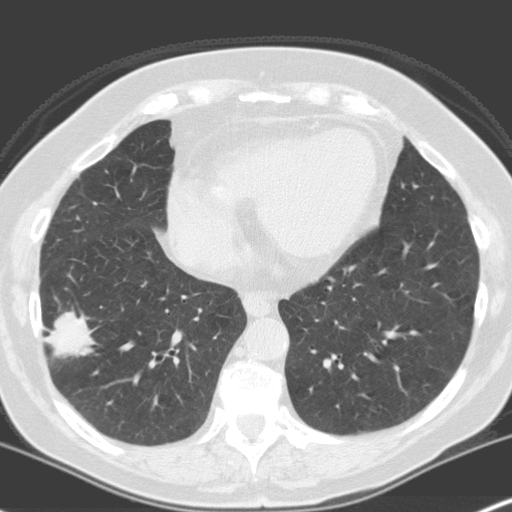
Low-dose screening chest CT, one axial slice; position 65 of 160 along the scan axis; 120 kVp; lung window (W 1500 / L -600 HU); 3.2 mm slice thickness; 512 × 512 image matrix.
Structures marked on this image (outlined manually by an expert reader):
- lesion 1 (tumor, lower lobe of right lung): bounding box (x1, y1, x2, y2) in pixels: (45, 311, 94, 358)